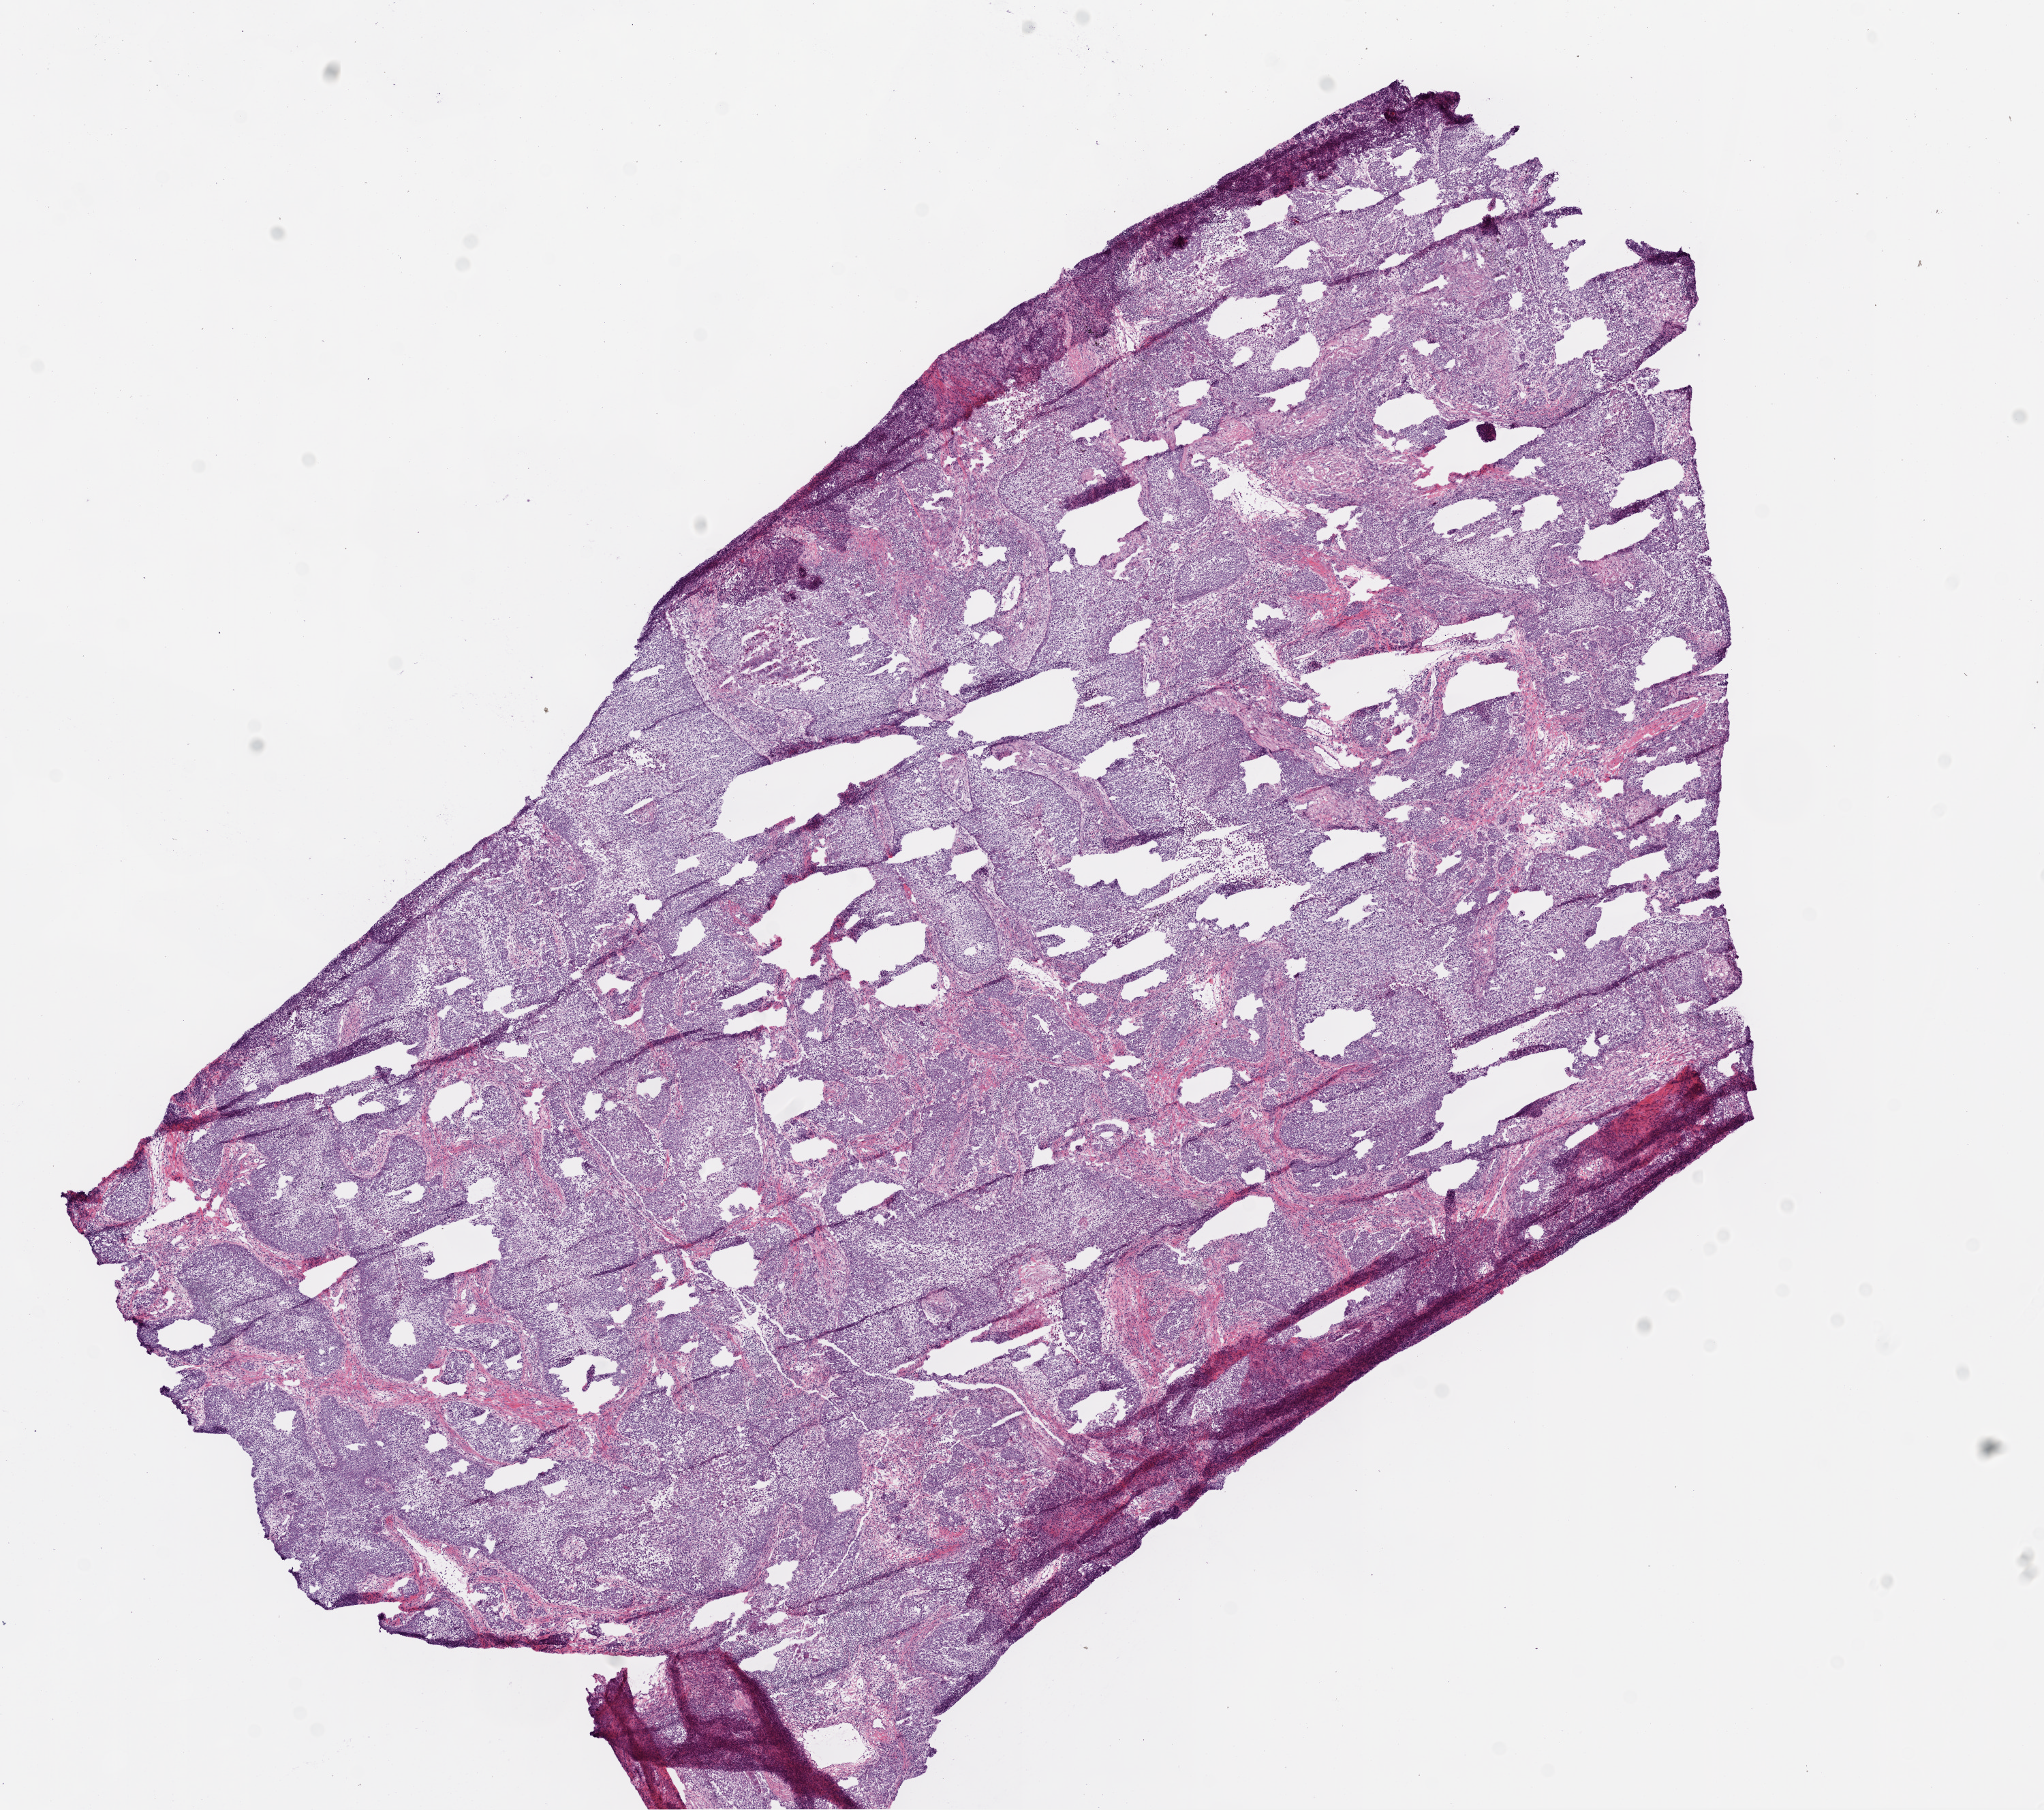
Whole-slide histology image, Hematoxylin and eosin (H&E) stained — low-resolution overview of the scanned area, about 12.0 x 10.7 mm (slide scanned at 20x), frozen section, sample: primary tumour, lung. Male patient; age at initial diagnosis 73 years. Composition of this section per pathologist review: tumour cells 92%, tumour nuclei 85%, normal cells 0%, stromal cells 5%, necrosis 3%.
- TNM: T2 N0 M0
- AJCC pathologic stage: IB
- diagnosis: Squamous cell carcinoma, NOS (upper lobe, lung)